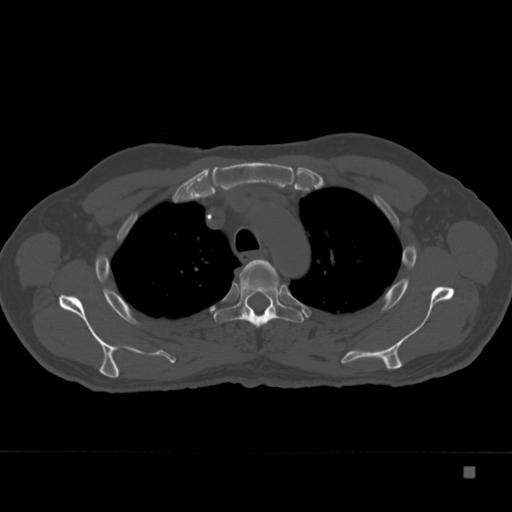
CT including the spine, one axial slice; position 275 of 332 along the scan axis; 120 kVp; bone window (W 1800 / L 400 HU); 1.5 mm slice thickness; 512 × 512 image matrix, field of view 389 × 389 mm. Patient: male, 72 years. Case-level facts recorded for this patient, not image findings: primary cancer: skeletal.
Outlined on this slice (semi-automatically segmented with operator editing):
- T3 vertebra: bounding box [x1, y1, x2, y2] px = [239, 260, 279, 293]
- T4 vertebra: [213, 260, 304, 328]